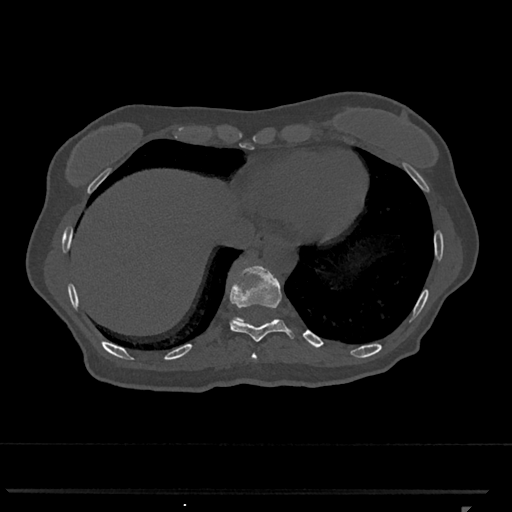
CT including the spine, one axial slice; reconstruction kernel Br40s/3; 120 kVp; bone window (W 1800 / L 400 HU); 0.5 mm slice thickness; 512 × 512 image matrix, field of view 380 × 380 mm. Patient: female, 62 years. Case-level facts recorded for this patient, not image findings: primary cancer: renal.
Structures marked on this image (semi-automatic segmentation, software-assisted and operator-edited):
- T10 vertebra: box from (x=230, y=263) to (x=294, y=342) px
- T11 vertebra: (x=233, y=307)–(x=273, y=322)
- T9 vertebra: (x=251, y=353)–(x=257, y=360)